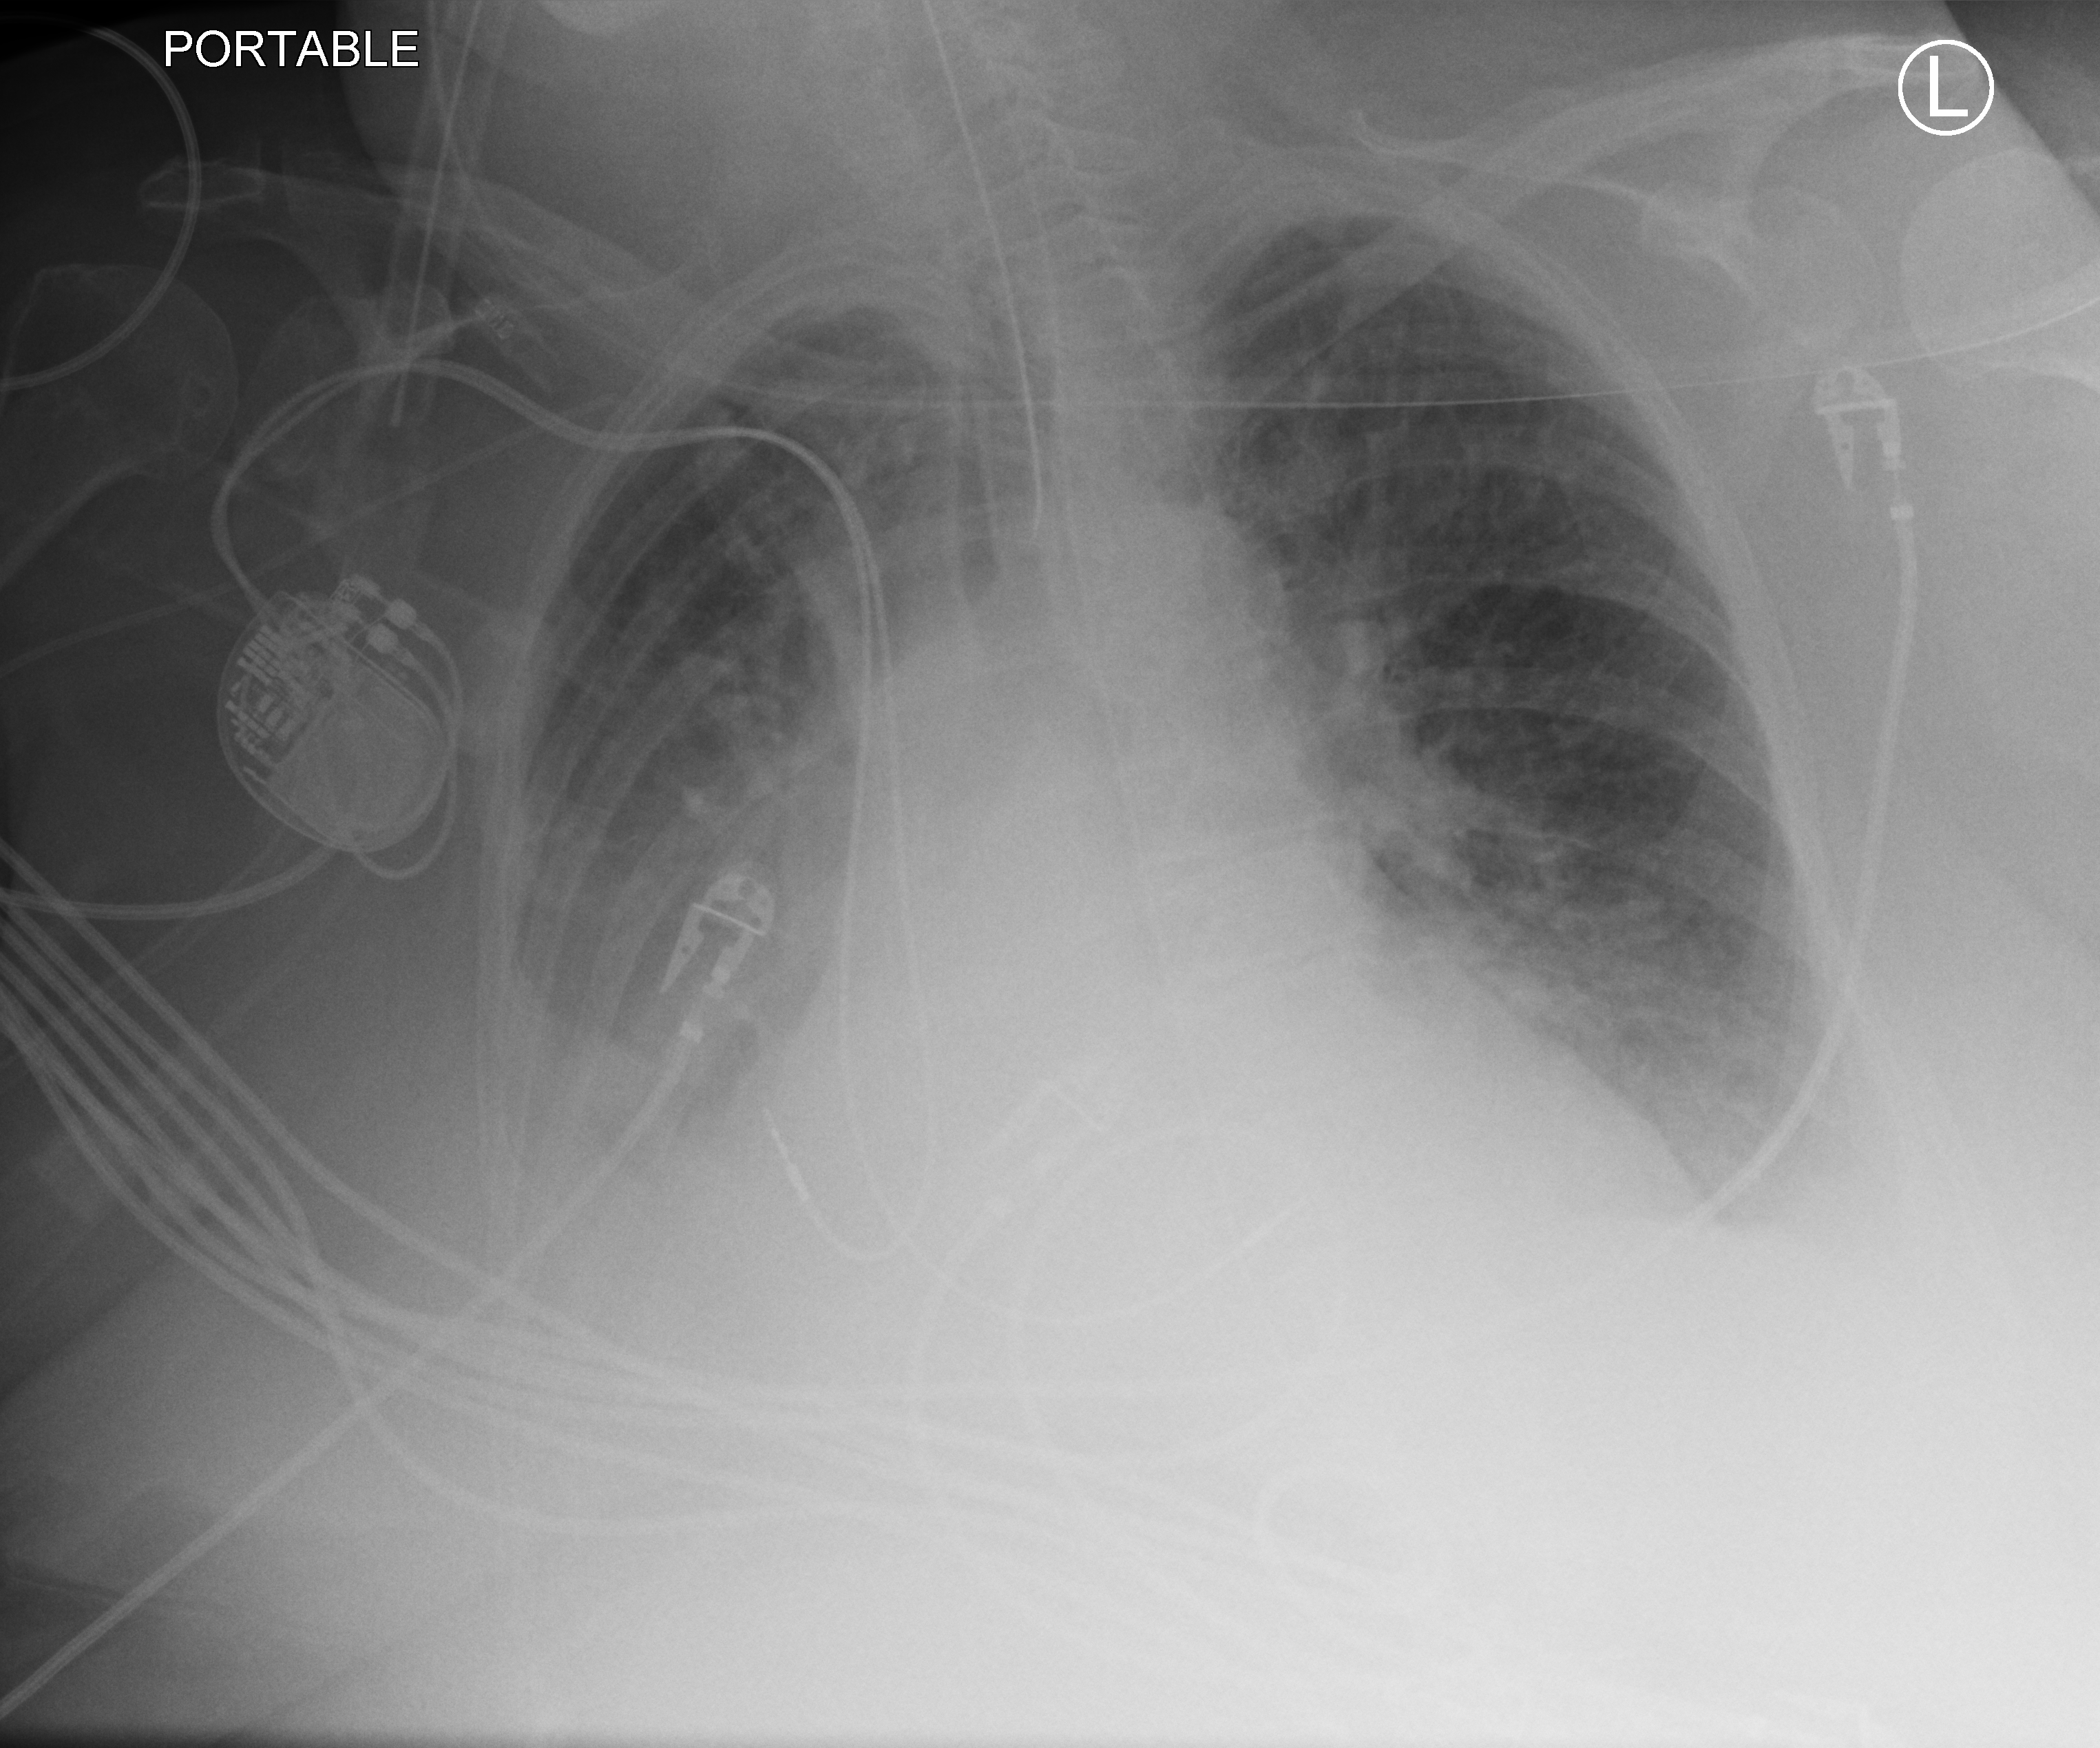
Portable chest radiograph, anteroposterior (AP) projection. Patient hospitalised with COVID-19; female, aged 75–90 years.
From the hospital-stay record, not from the radiograph (when in the stay this image was taken is not recorded):
- length of hospital stay: 21 days
- mechanically ventilated during this hospital stay: yes